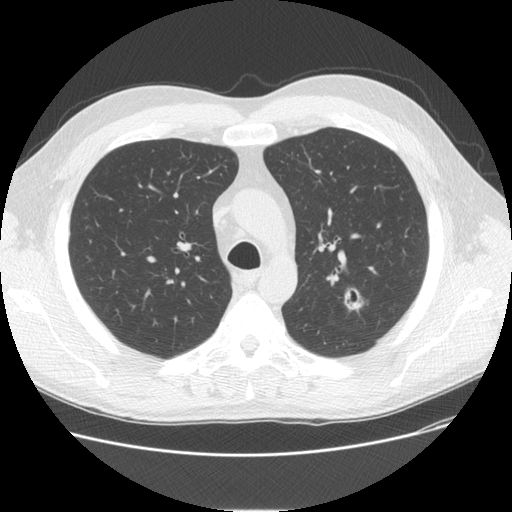
Chest CT (low-dose screening protocol), one axial image, third annual screen, lung window (W 1500 / L -600 HU), standard (soft-tissue) reconstruction kernel (STANDARD), slice 39 of 150 in the series. Male, age 57 years at enrolment.
Lesion marked by an expert reader, box from (x=323, y=283) to (x=374, y=322) px. Reader record for this screening exam (exam-level; its link to the box is not recorded): non-calcified nodule or mass ≥4 mm, left upper lobe, 17 × 13 mm, spiculated (stellate) margins, mixed attenuation, pre-existing on the prior screen: yes; interval growth: yes. Official screen result: positive, other. Participant outcome: lung cancer diagnosed 64 days after this screen — adenosquamous carcinoma, left upper lobe, poorly differentiated (G3), stage IA (AJCC 6th edition), 15 mm at pathology.